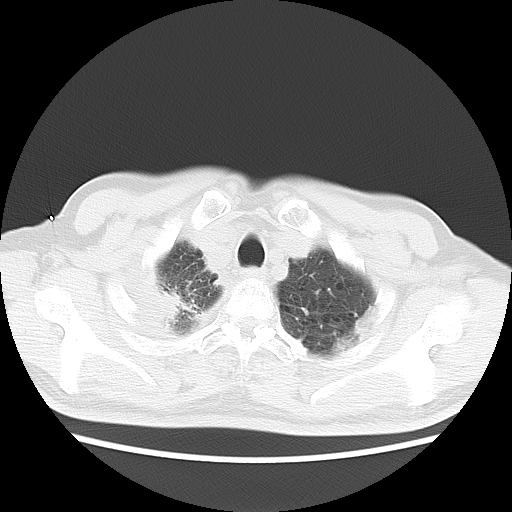
Chest CT, one axial slice; slice 18 of 20 in the series (ordered by position); reconstruction kernel LUNG; 120 kVp; lung window (W 1500 / L -600 HU); 5 mm slice thickness; 512 × 512 image matrix, field of view 350 × 350 mm. Patient: male, 75 years. Case-level facts recorded for this patient, not image findings: clinical TNM (as recorded): T1c N1 M1.
Structures marked on this image (rectangle marked by the reading radiologist):
- lung tumour (recorded histology: adenocarcinoma): bounding box <157,286,184,322> (left, top, right, bottom; pixels)